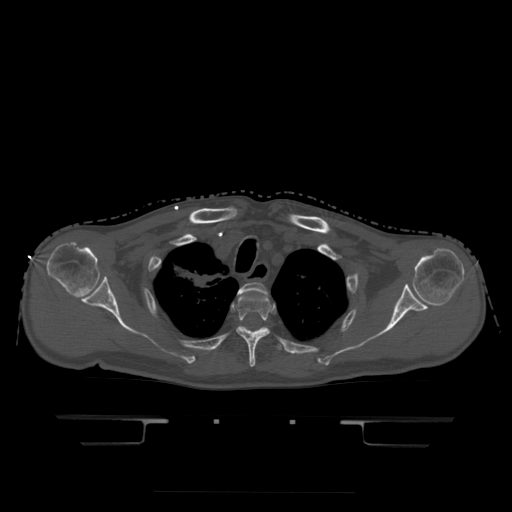
CT including the spine, one axial slice; position 370 of 522 along the scan axis; bone window (W 1800 / L 400 HU); 1.25 mm slice thickness; 512 × 512 image matrix, field of view 436 × 436 mm. Patient age 68 years. Case-level facts recorded for this patient, not image findings: primary cancer: urothelial.
Outlined on this slice (semi-automatic segmentation, software-assisted and operator-edited):
- T2 vertebra: bounding box [x1, y1, x2, y2] px = [238, 283, 269, 296]
- T3 vertebra: [237, 290, 274, 368]
- T4 vertebra: [238, 327, 283, 351]